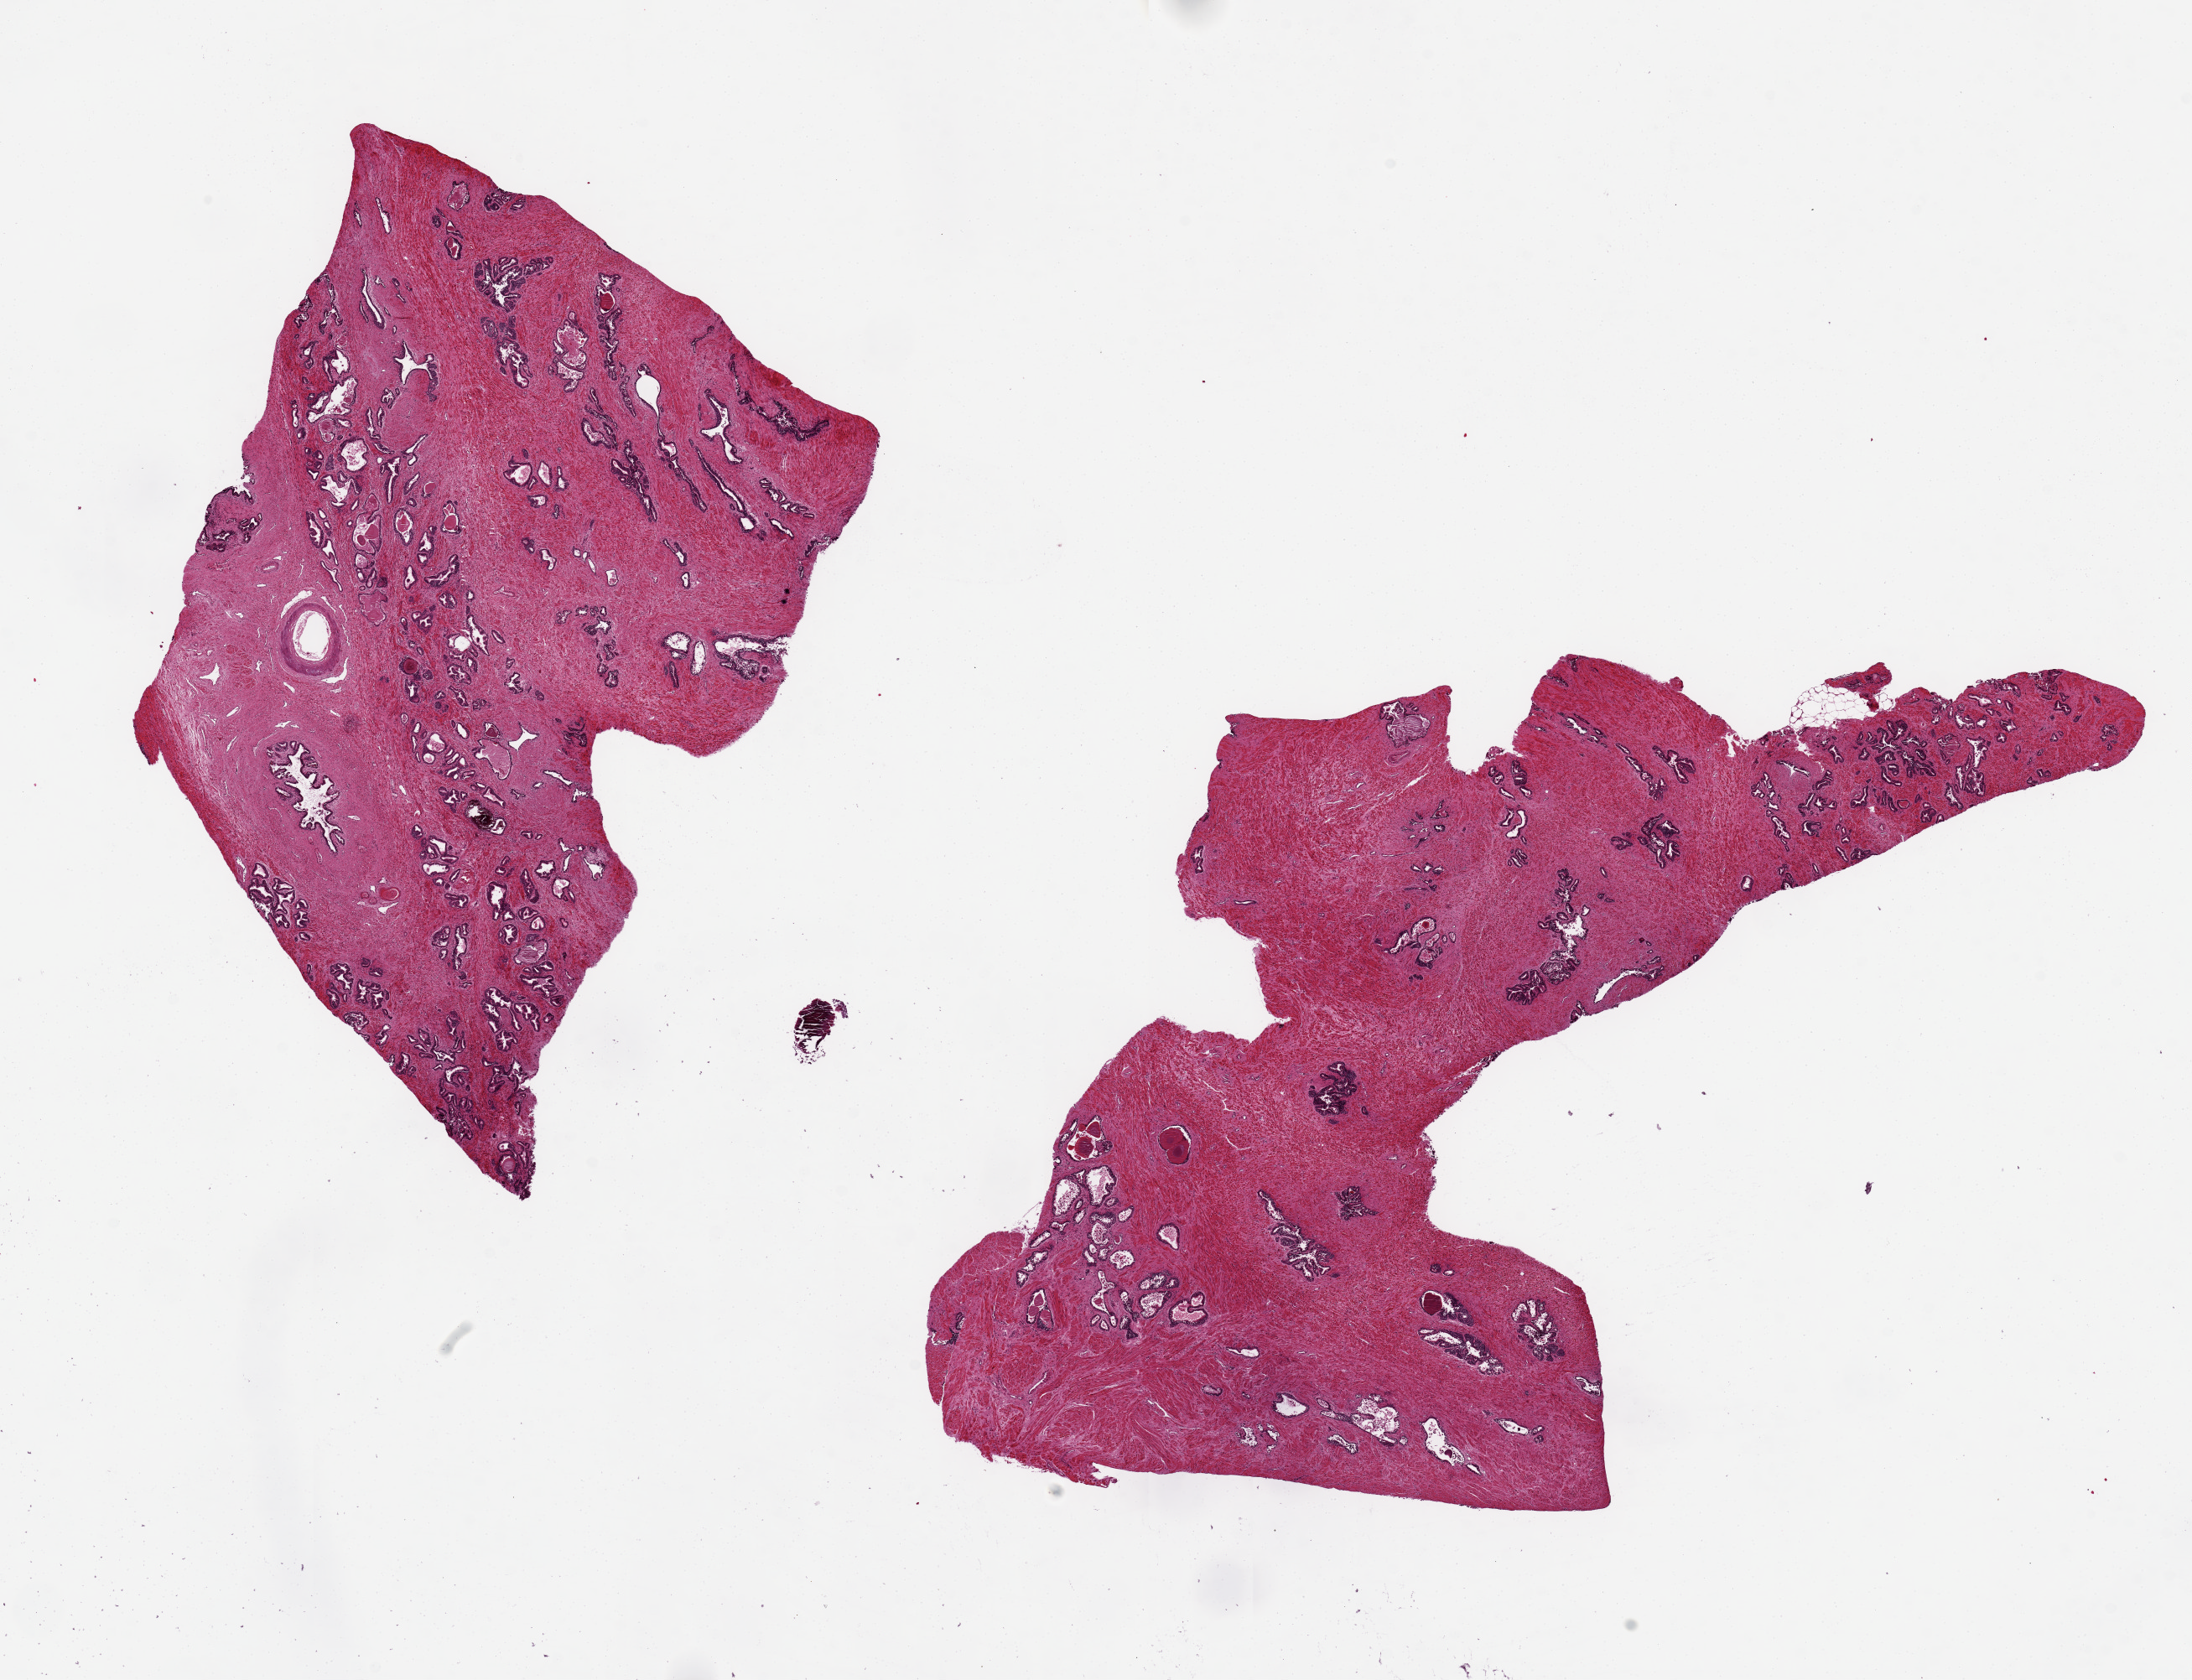
Digitized haematoxylin and eosin-stained section, shown as a low-resolution overview of the whole scanned area (about 20.7 x 15.8 mm), PAXgene-fixed, paraffin-embedded tissue, target tissue: prostate, tissue donor sample. Donor sex: male.
Review note (as recorded): 2 aliquots, patchy glandular hyperplasia.